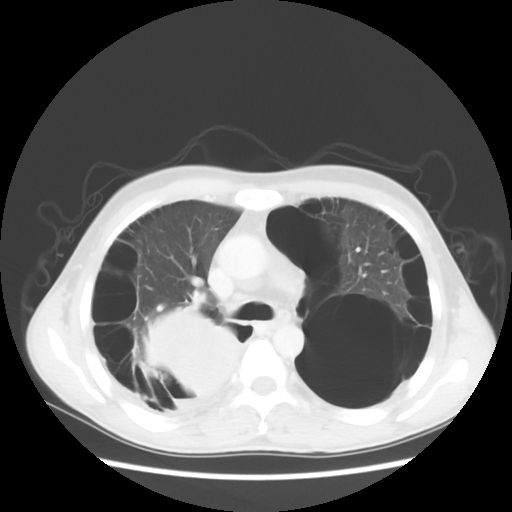
Chest CT, one axial slice; slice 36 of 56 in the series (ordered by position); reconstruction kernel STANDARD; lung window (W 1500 / L -600 HU); 5 mm slice thickness; 512 × 512 image matrix, field of view 351 × 351 mm. Patient: male, 41 years. From the clinical record (not read from this slice): clinical TNM (as recorded): T4 N0 M1a.
Annotated regions visible in this slice (rectangle marked by the reading radiologist):
- lung tumour (recorded histology: large cell carcinoma): bounding box (x1, y1, x2, y2) in pixels: (133, 308, 240, 414)